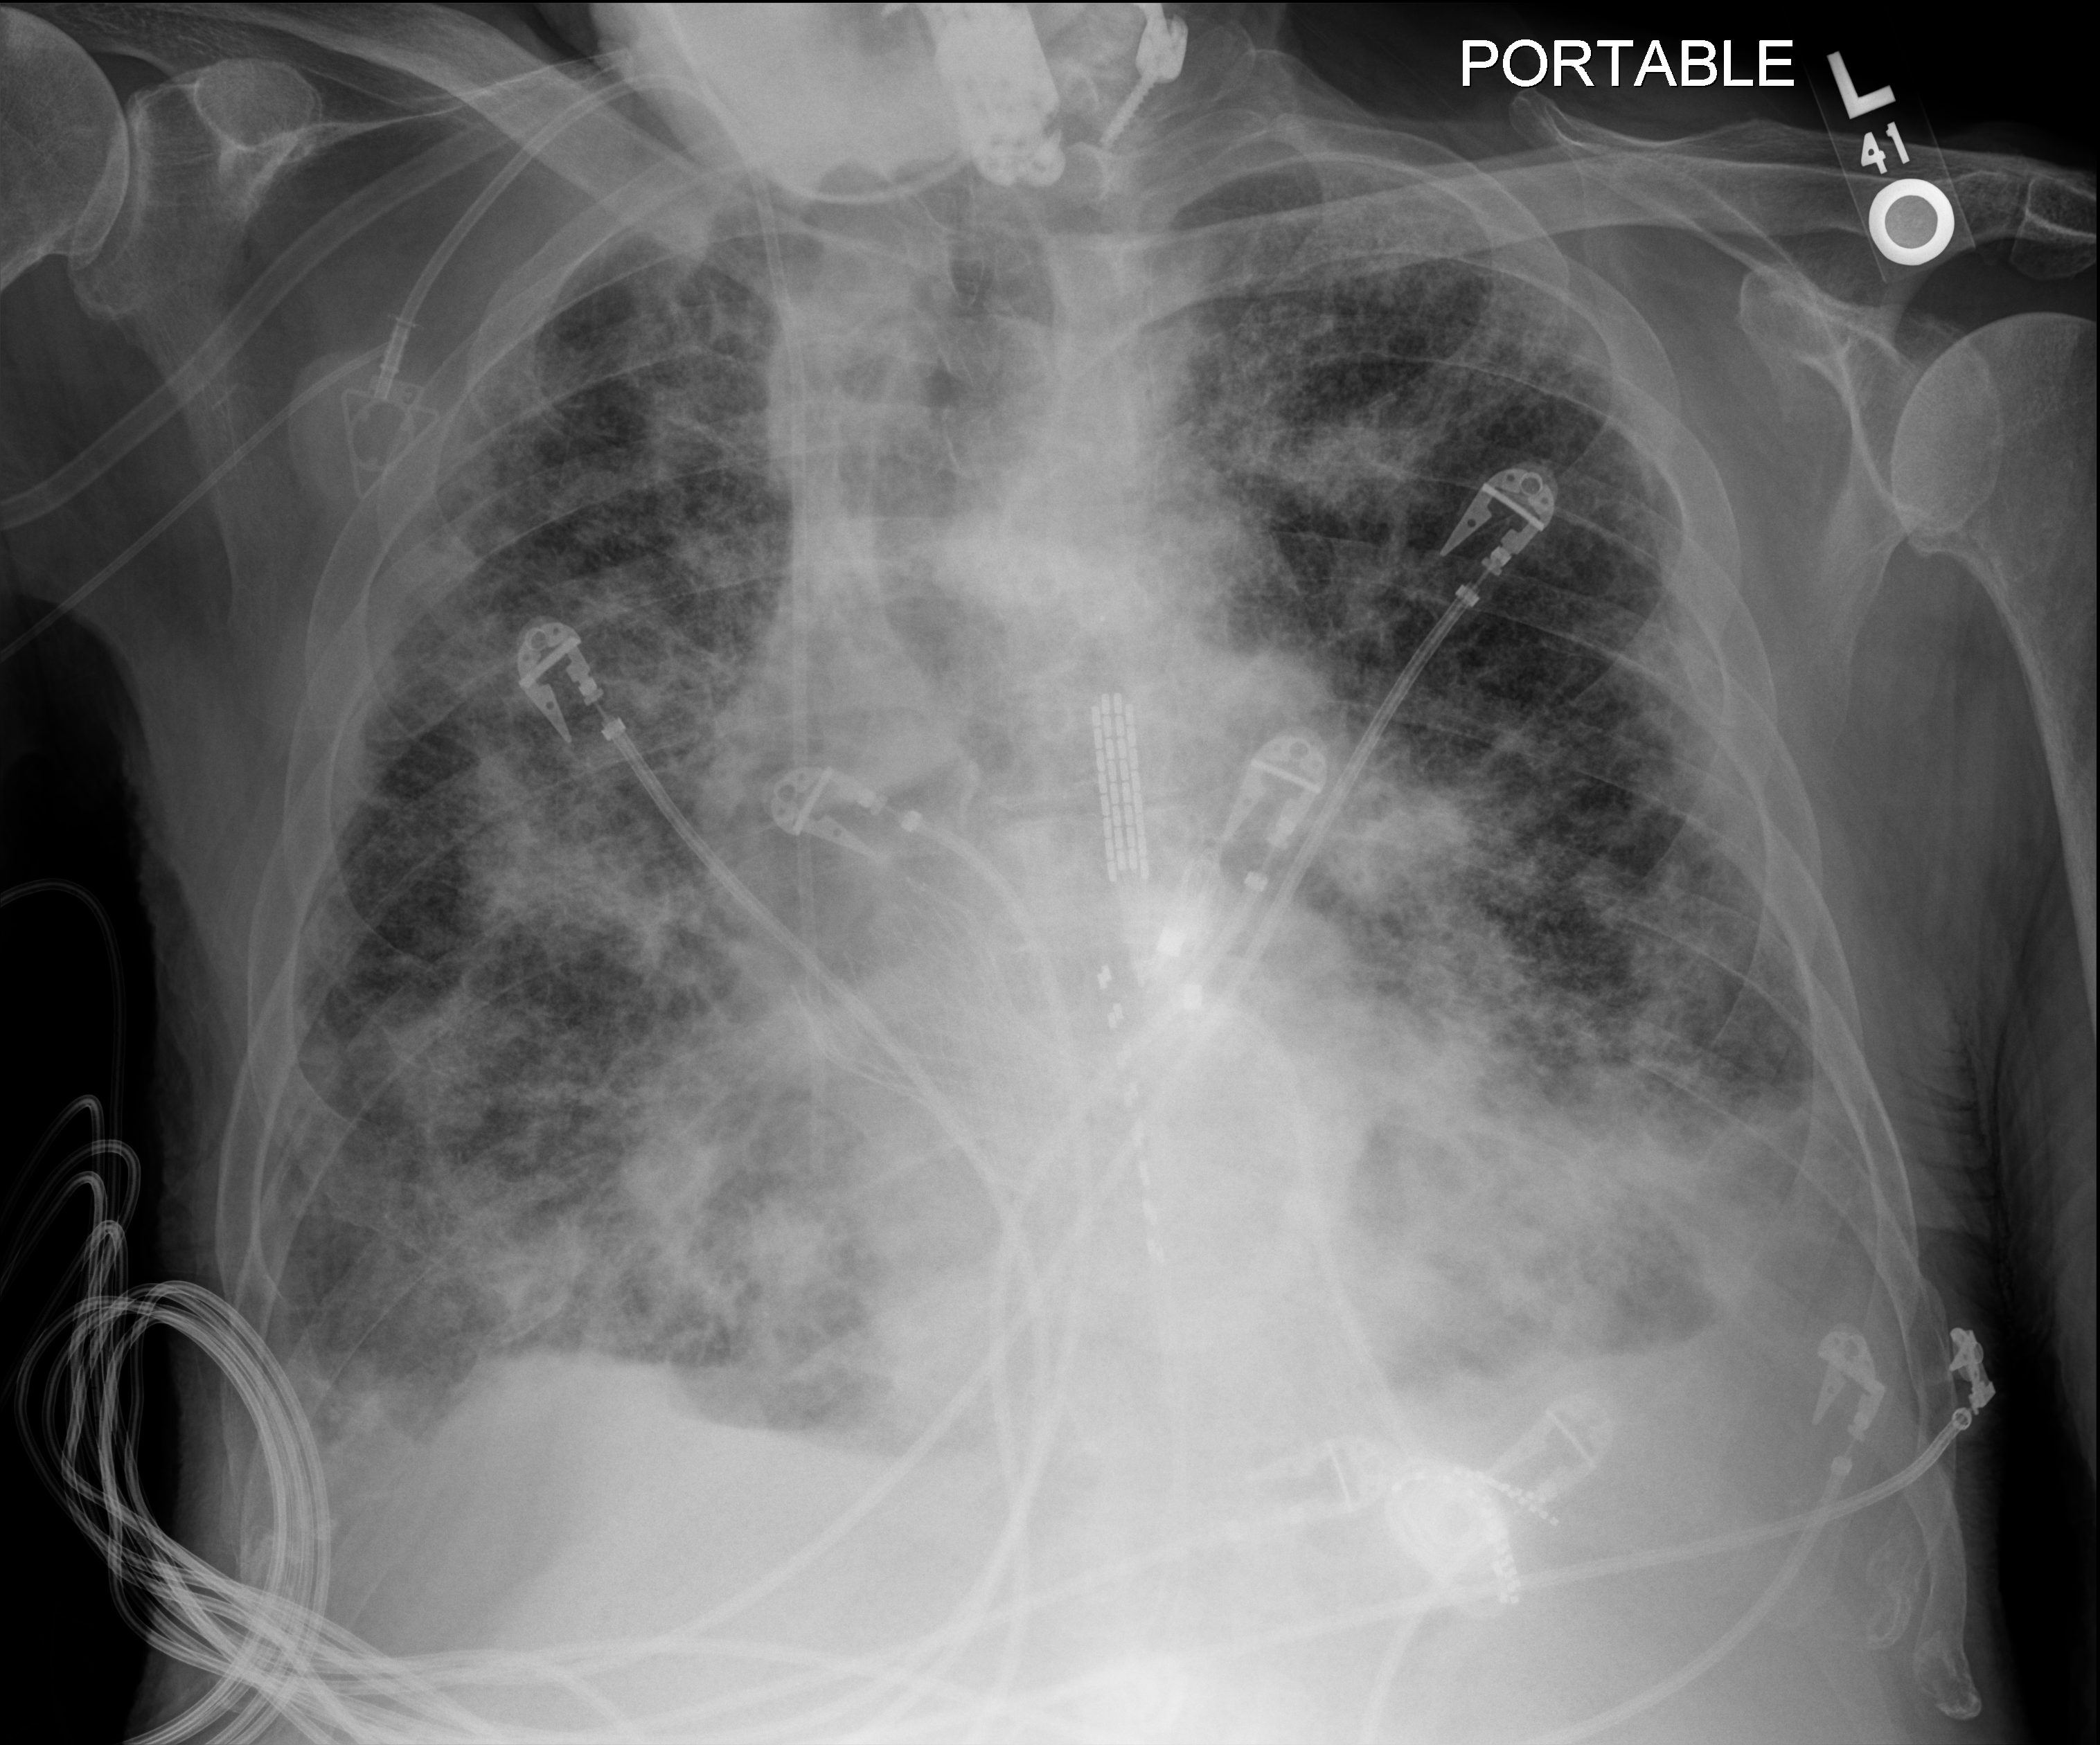
Chest X-ray (portable); anteroposterior (AP) projection. Patient hospitalised with COVID-19; male, aged 75–90 years.
Hospital-stay facts (about this admission, not read from this image; timing relative to this image not recorded):
- mechanically ventilated during this hospital stay: no
- admitted to intensive care during this hospital stay: yes
- other chronic lung disease (admission record): yes